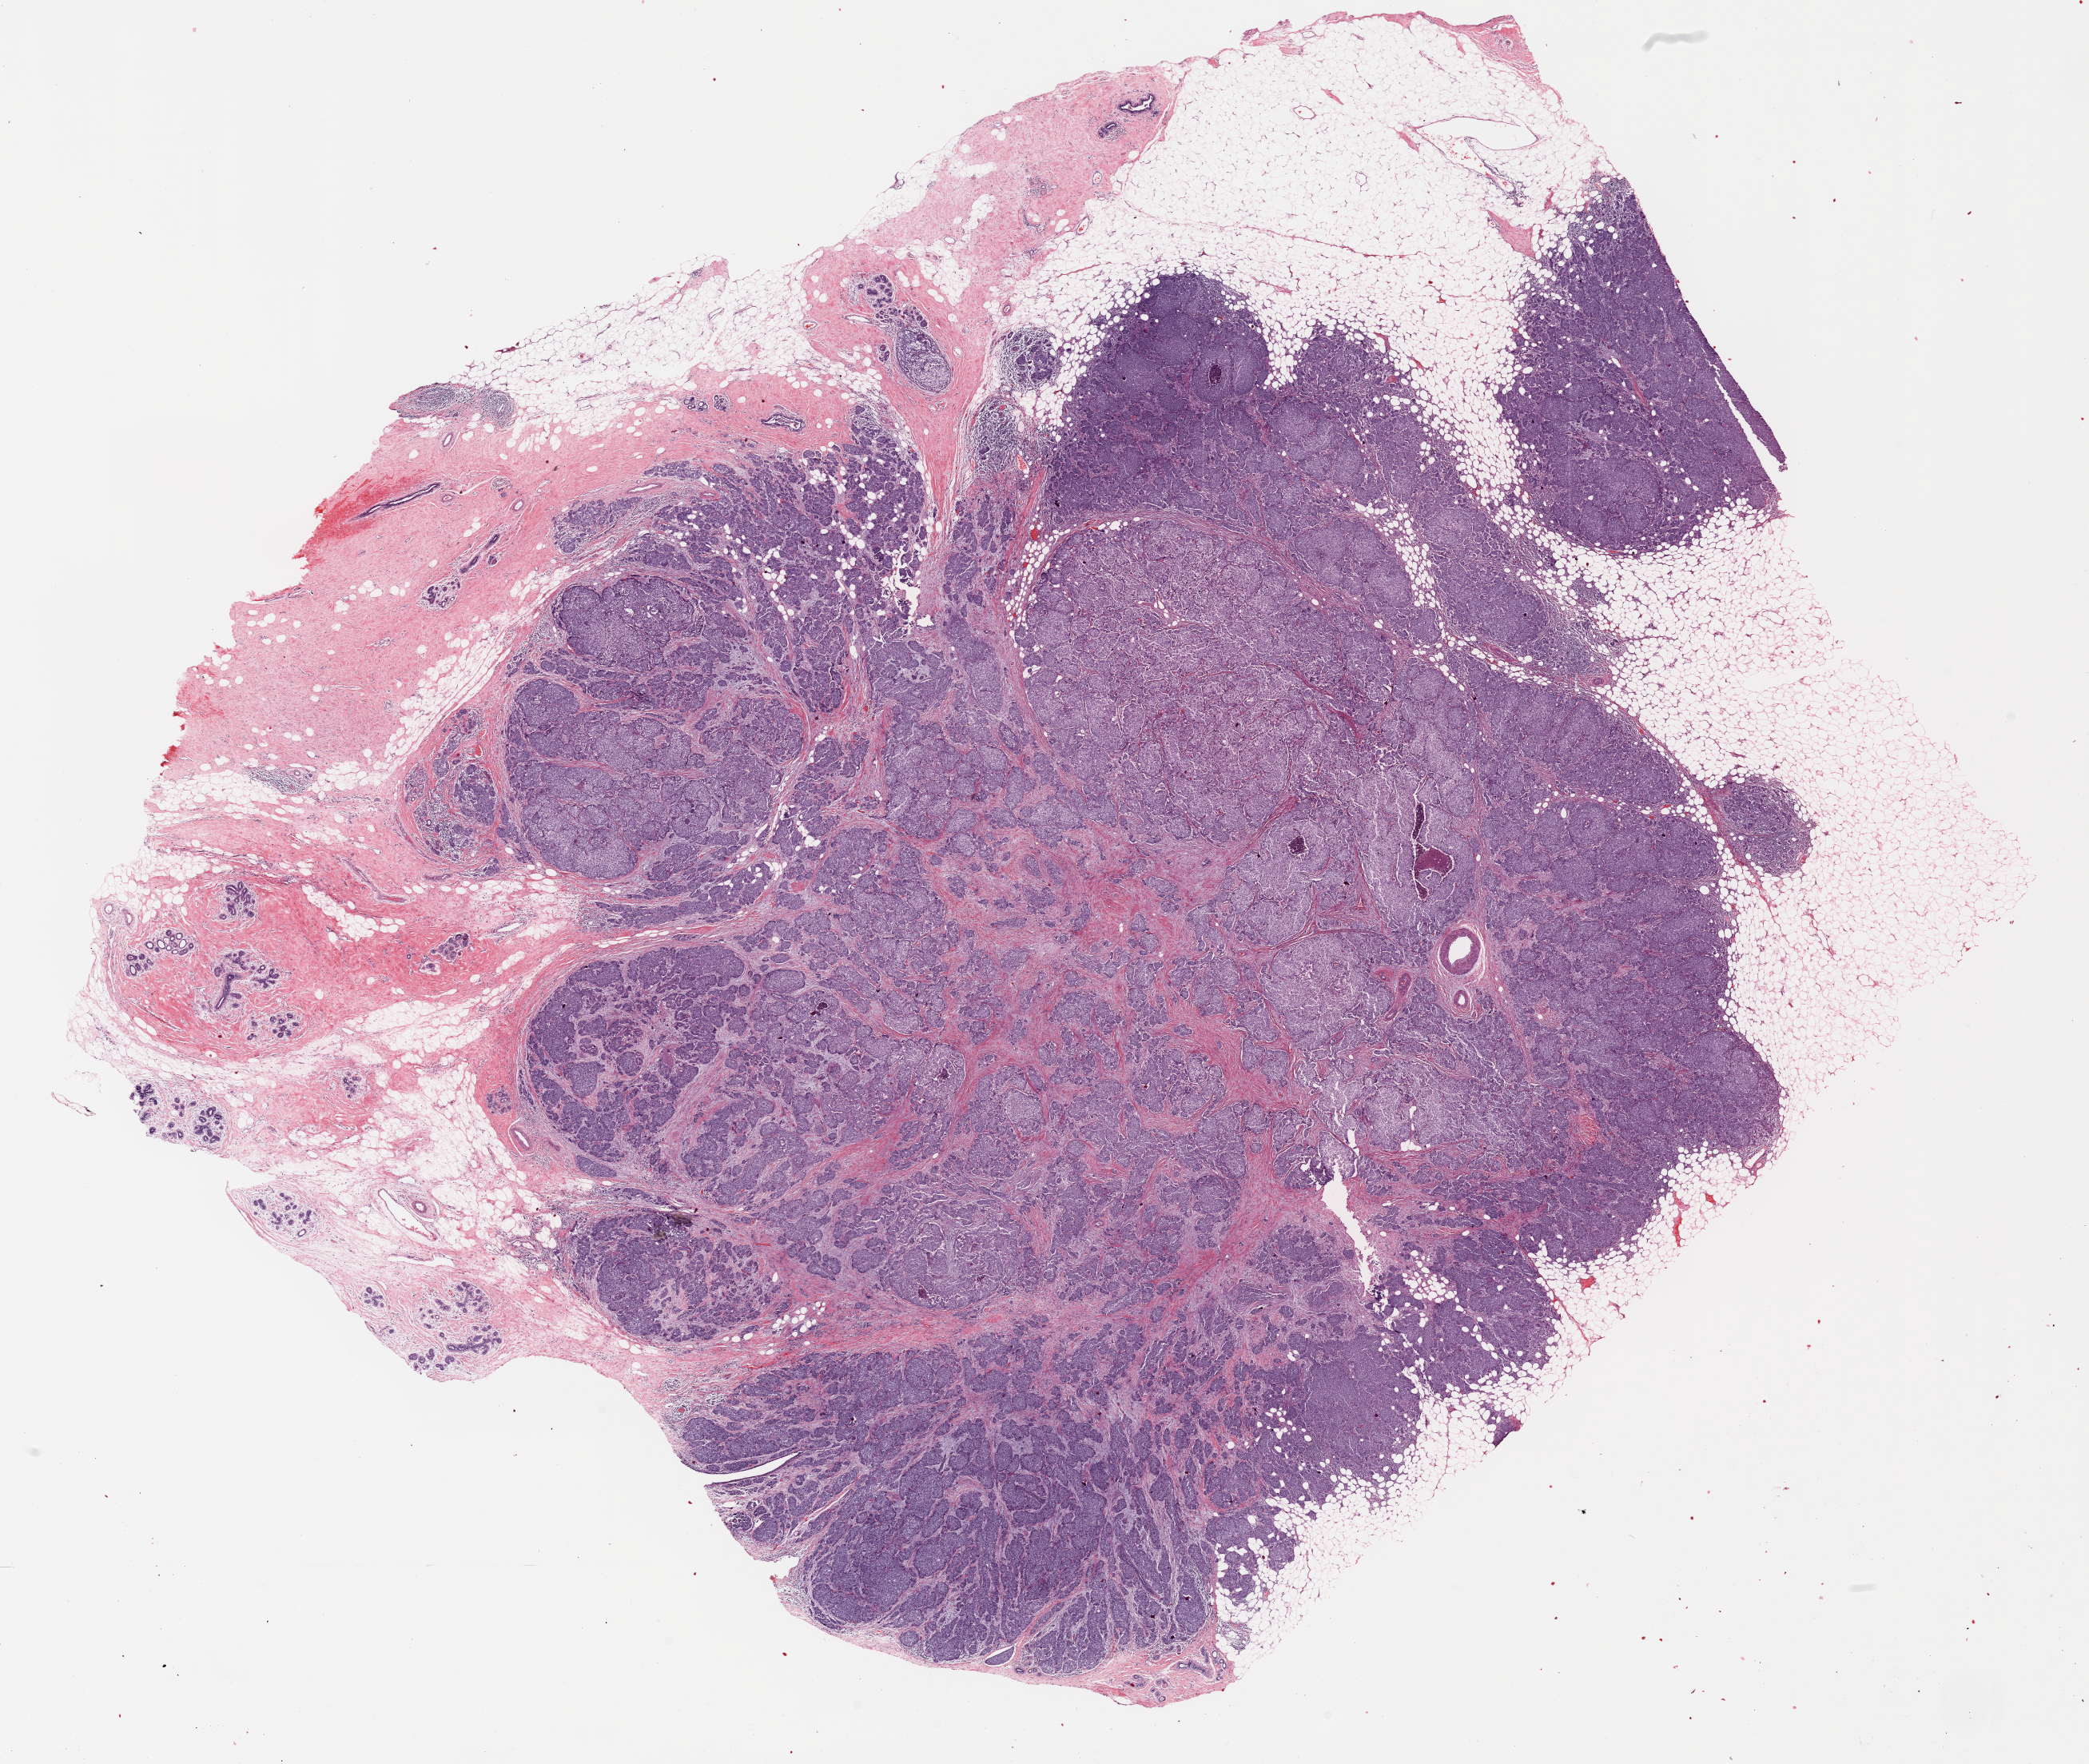
Whole-slide histology image, H&E-stained — whole scanned area (about 20.9 x 17.6 mm, from a 20x scan) shown as a low-resolution overview; FFPE section; sample: primary tumour, breast. Patient: female, age at initial diagnosis 42 years.
Pathologic diagnosis: Infiltrating duct carcinoma, NOS. AJCC pathologic stage: IIB (6th edition).